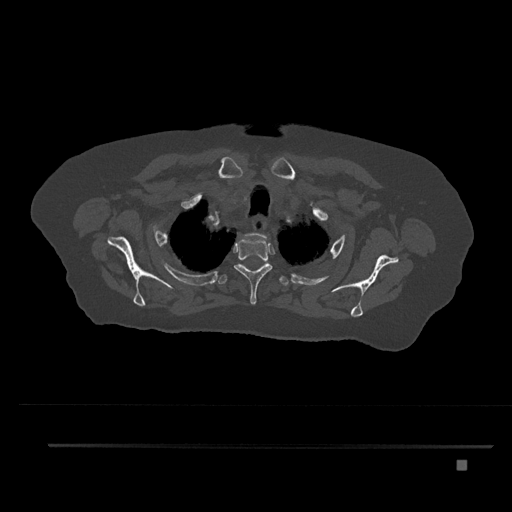
CT including the spine, one axial slice; position 665 of 797 along the scan axis; reconstruction kernel Br40s/3; 120 kVp; bone window (W 1800 / L 400 HU); 0.5 mm slice thickness; 512 × 512 image matrix. Female patient, age 76 years. From the clinical record (not read from this slice): primary cancer: lung; vertebrae with lytic lesions (as recorded): T11, L3.
Outlined on this slice (semi-automatically segmented with operator editing):
- T1 vertebra: bounding box <245,233,268,245> (left, top, right, bottom; pixels)
- T2 vertebra: <234,237,272,305>
- T3 vertebra: <219,262,289,285>